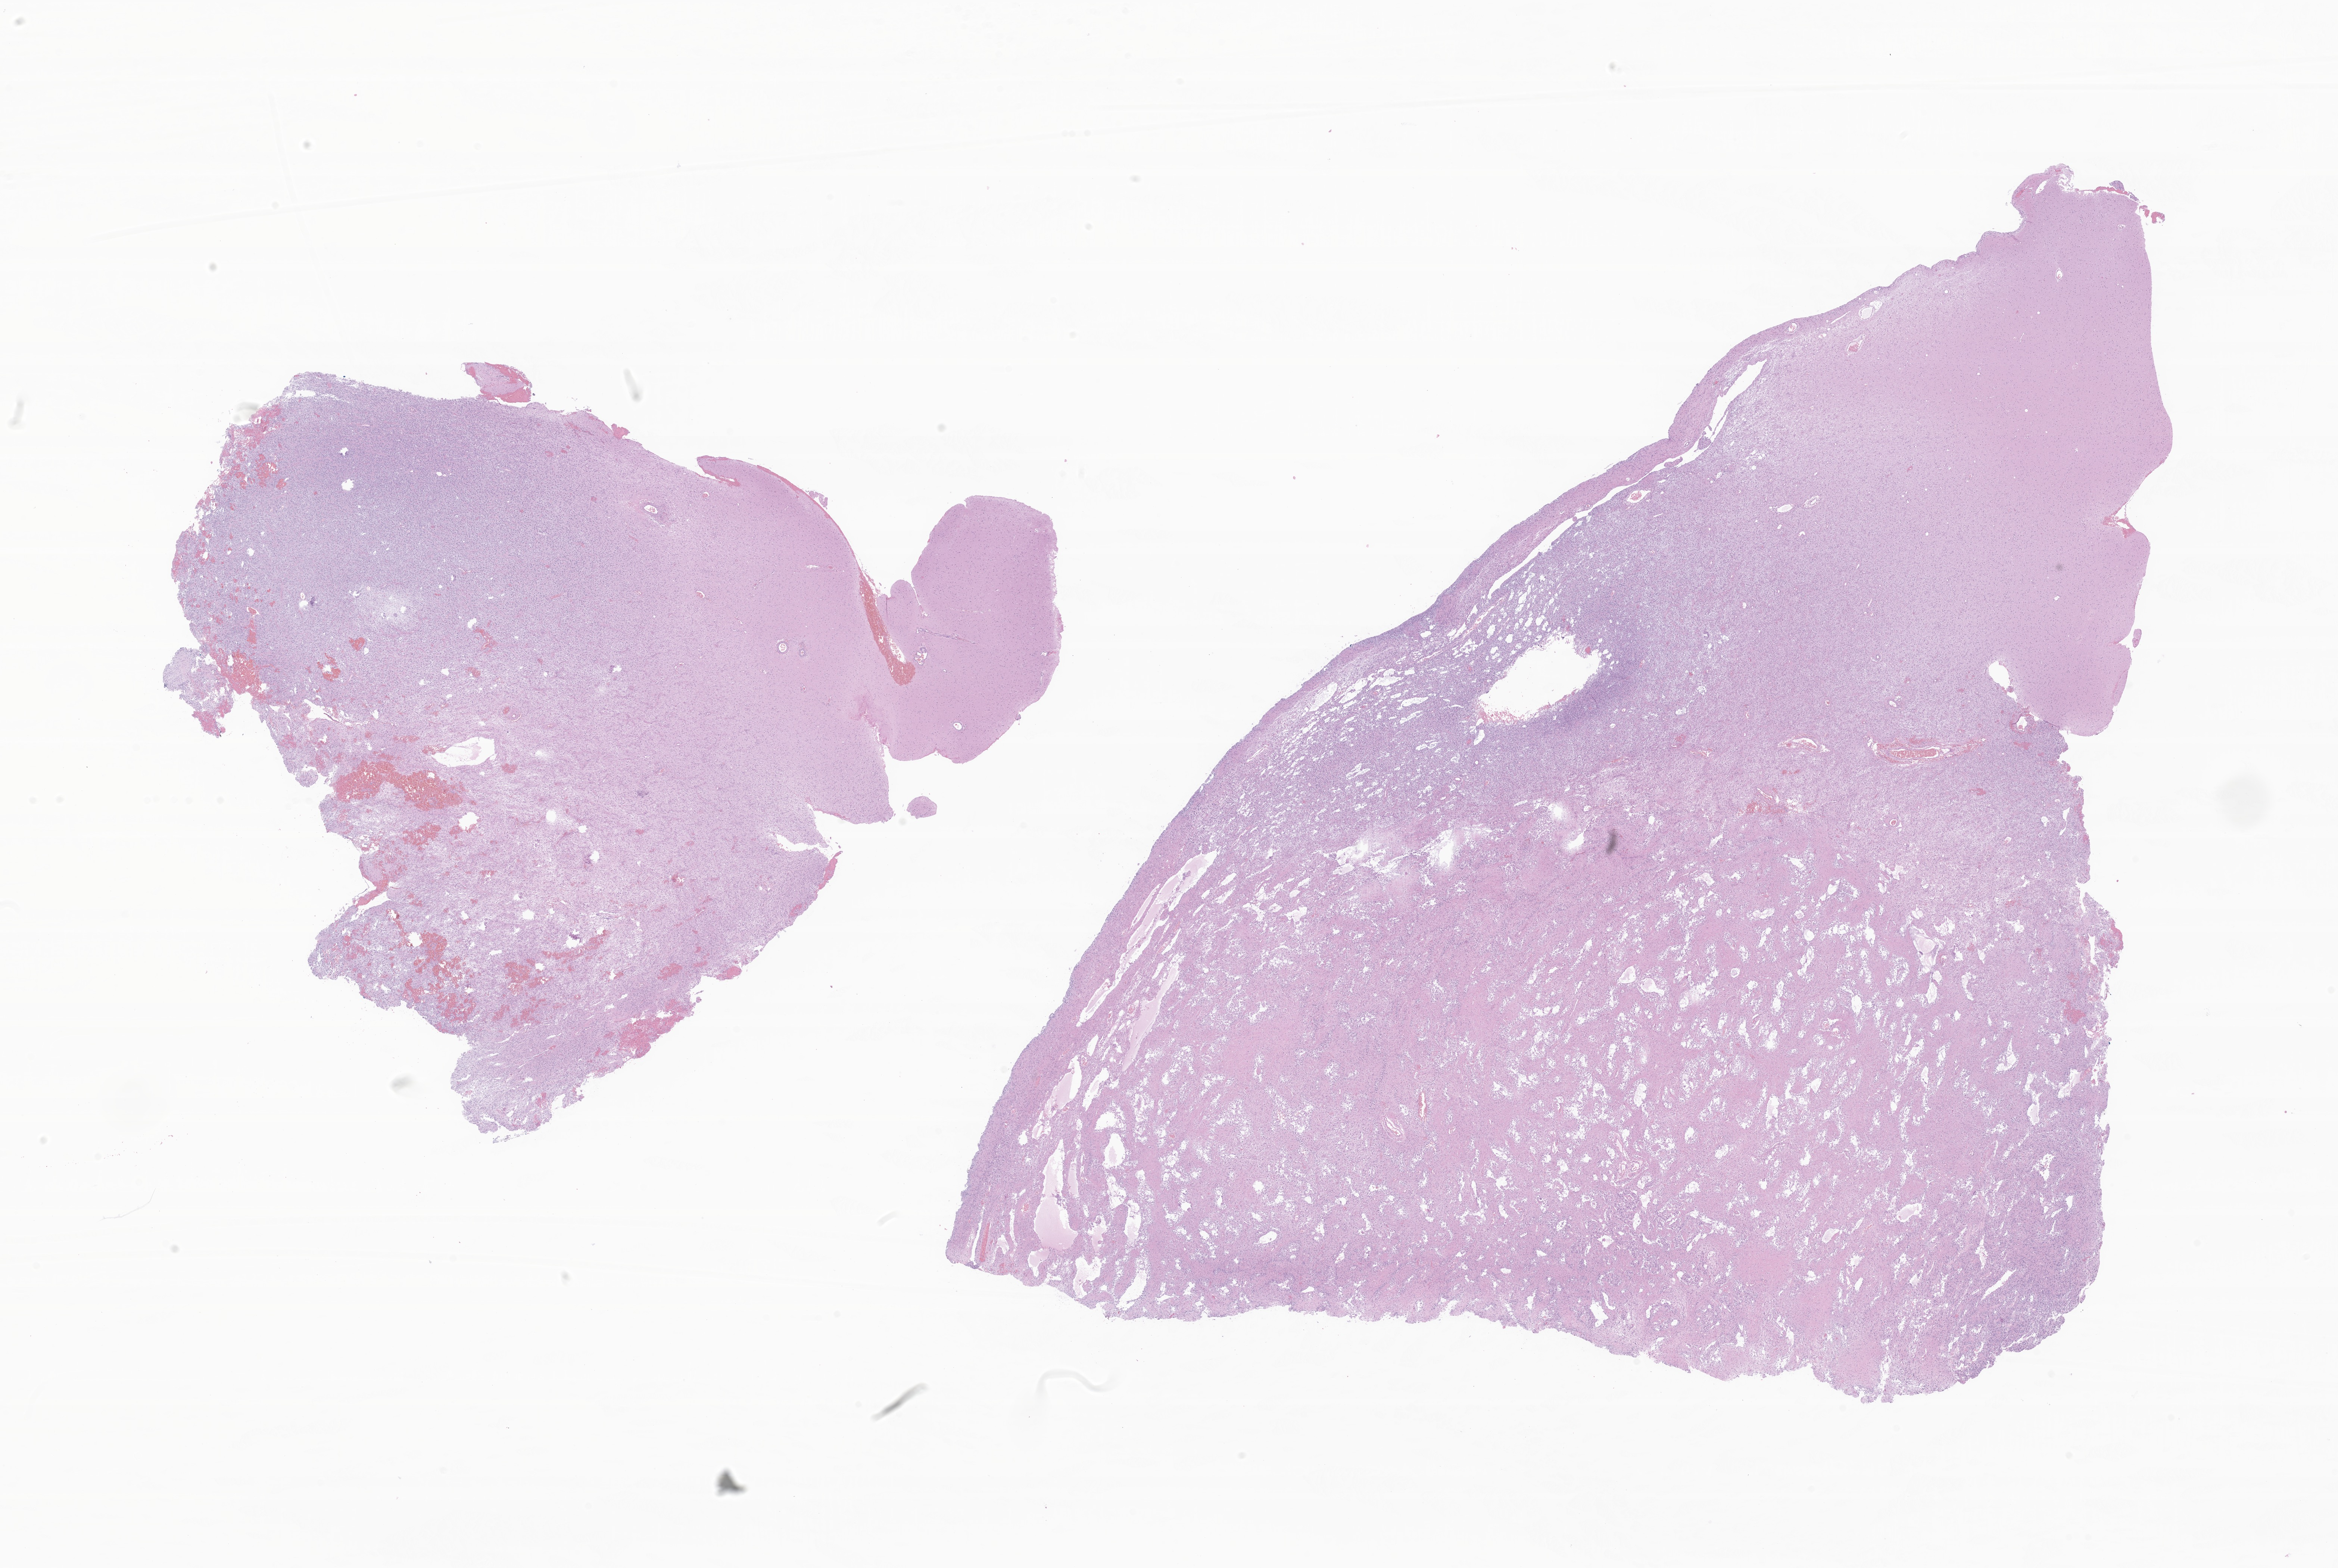
Digitized H&E-stained section of tumor tissue from the brain, whole scanned area (about 26.4 x 17.7 mm) shown as a low-resolution overview, FFPE section. Patient: female, age 185 months (15 years 5 months).
- recorded diagnosis: Neoplasm, uncertain whether benign or malignant